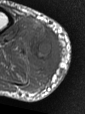
MRI of an extremity soft-tissue mass, one axial slice; MR volume resampled by the dataset authors to the PET/CT grid (not the native acquisition matrix); 85 × 114 image matrix, field of view 83 × 111 mm. Male patient. From the clinical record (not read from this slice): histological type: pleiomorphic liposarcoma; grade: high; site of the primary tumour: right calf.
Structures marked on this image (expert contour drawn on MRI and transferred to this co-registered scan by the dataset authors):
- gross tumour volume including surrounding oedema: bounding box [x1, y1, x2, y2] px = [26, 24, 62, 90]
- gross tumour volume (mass): [29, 34, 55, 61]